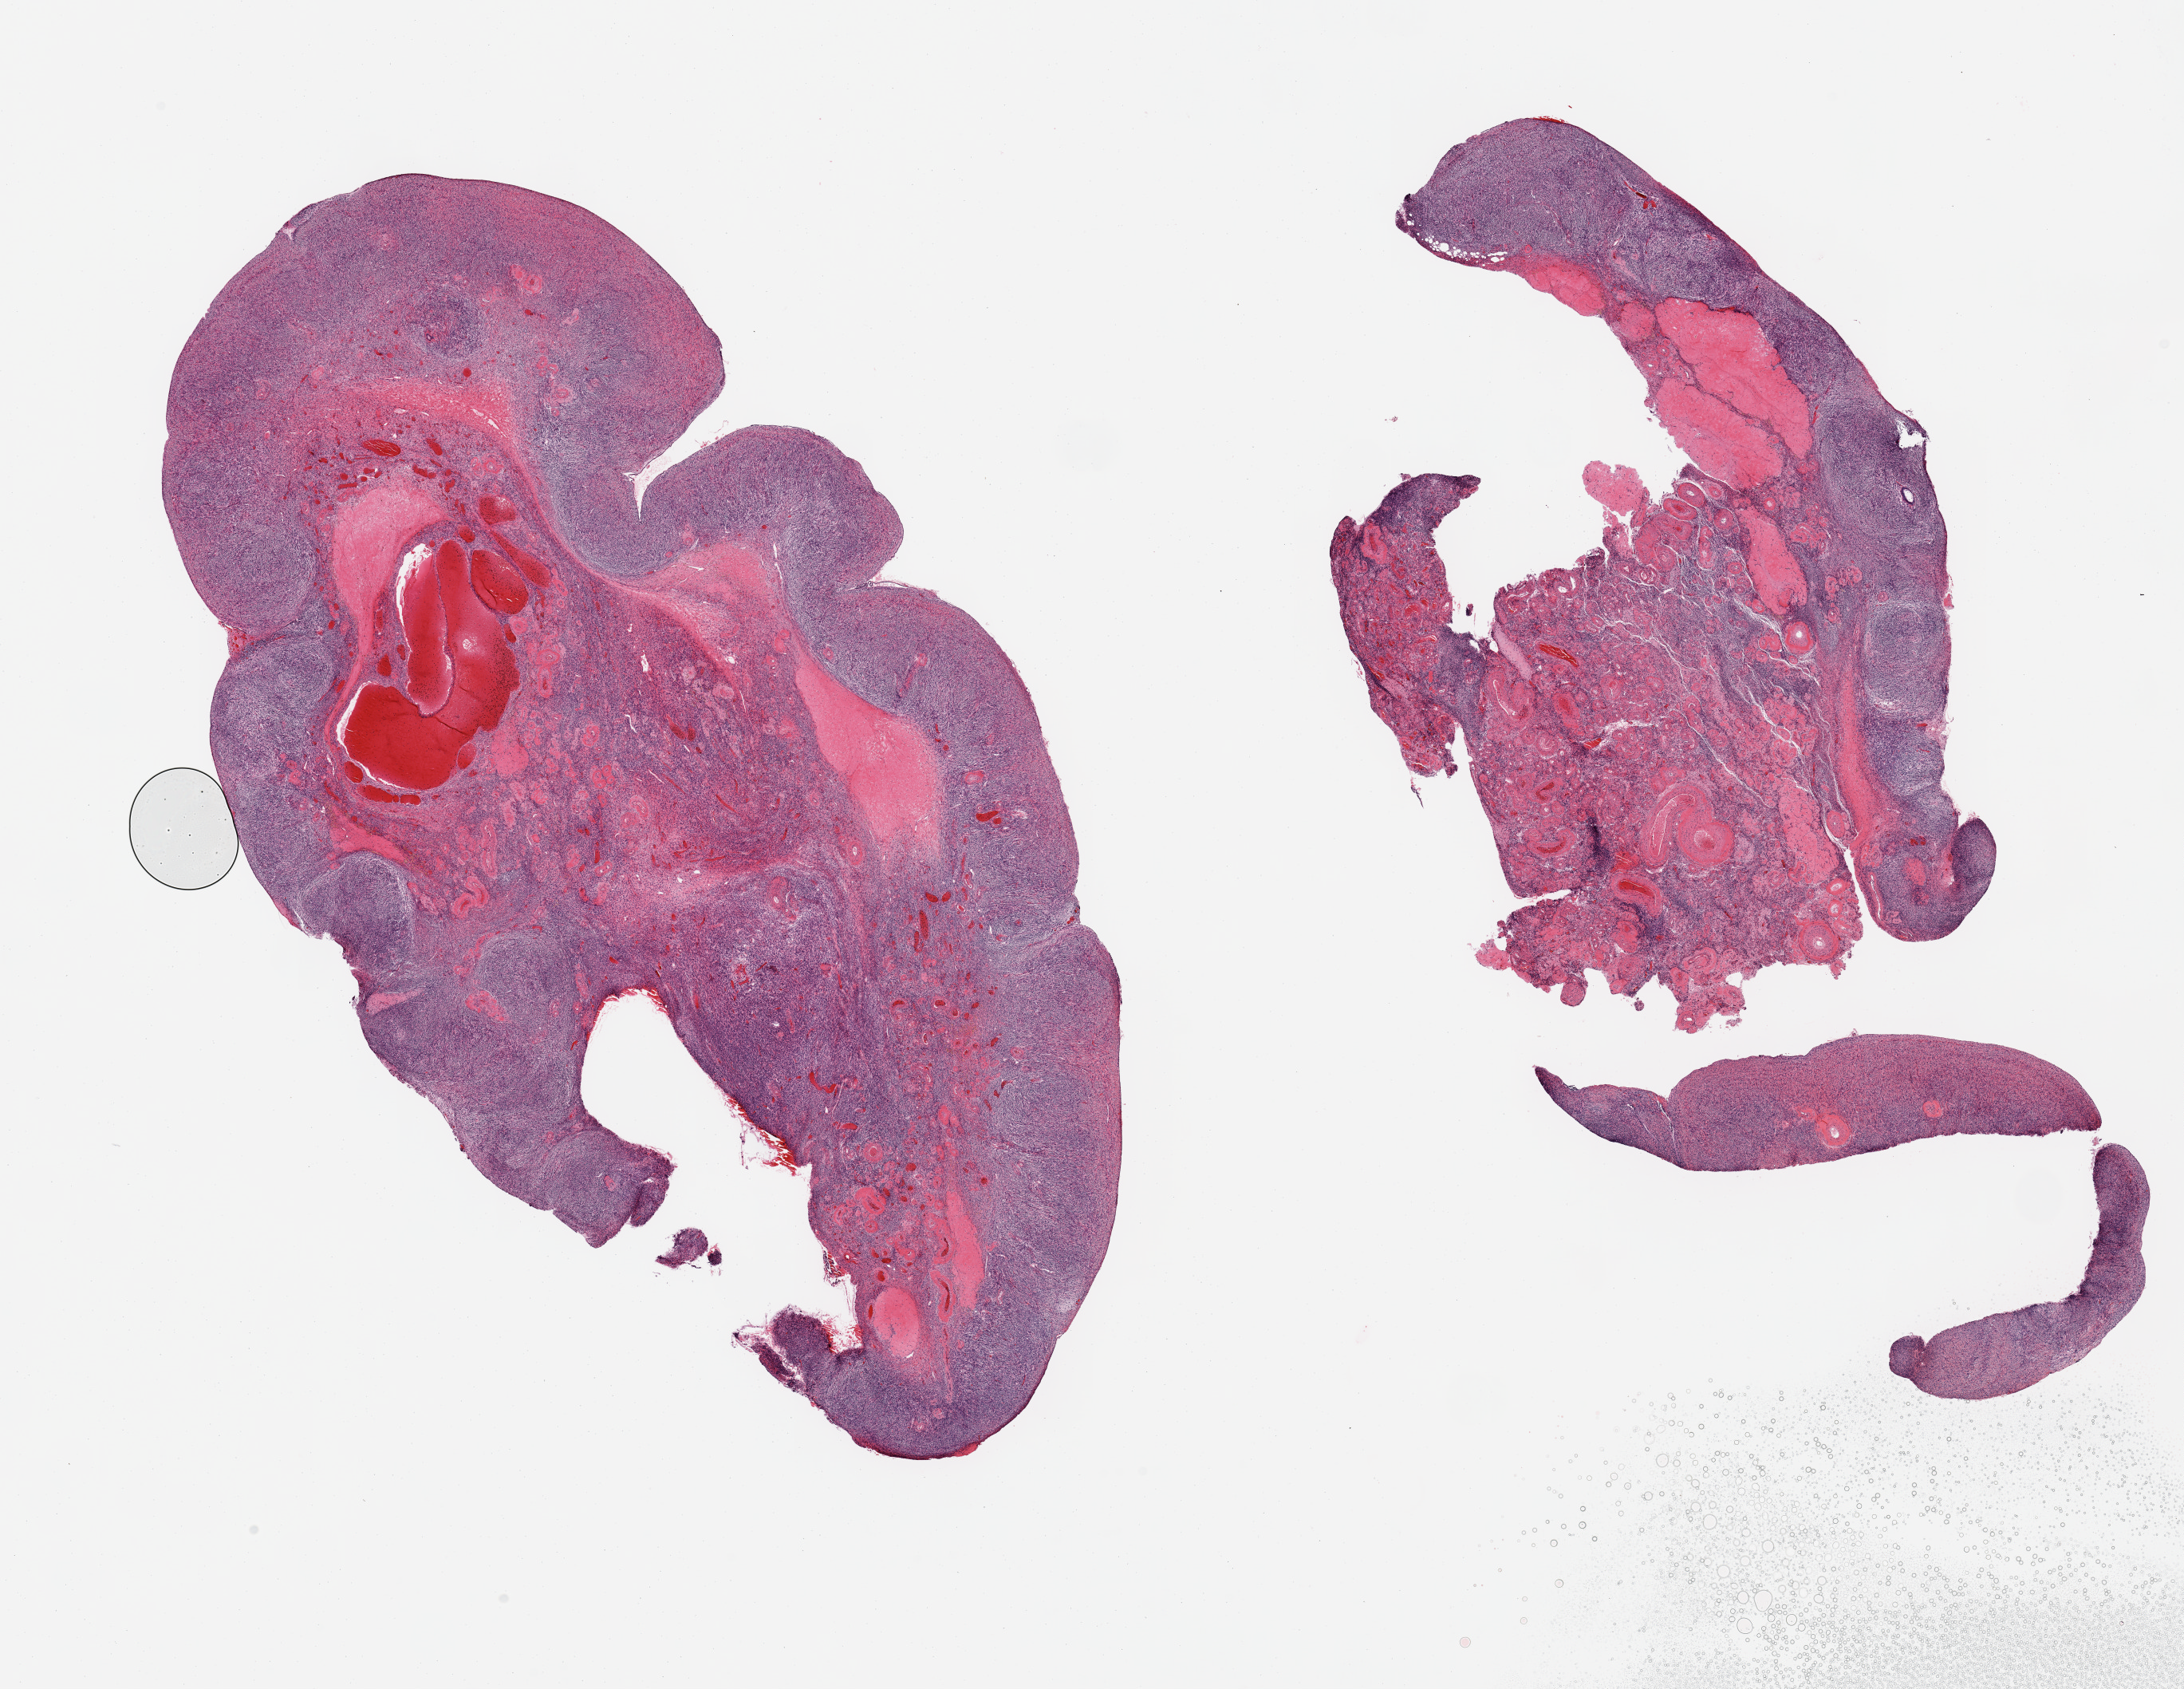
Digitized hematoxylin and eosin (H&E)-stained section — a low-resolution overview of the entire scanned area, about 21.7 x 16.7 mm (acquisition: 20x scan), PAXgene-fixed, paraffin-embedded tissue, section of ovary (target tissue), donor tissue sample. Donor sex: female.
Review note (as recorded): 2 pieces; atrophic with corpora albicans.